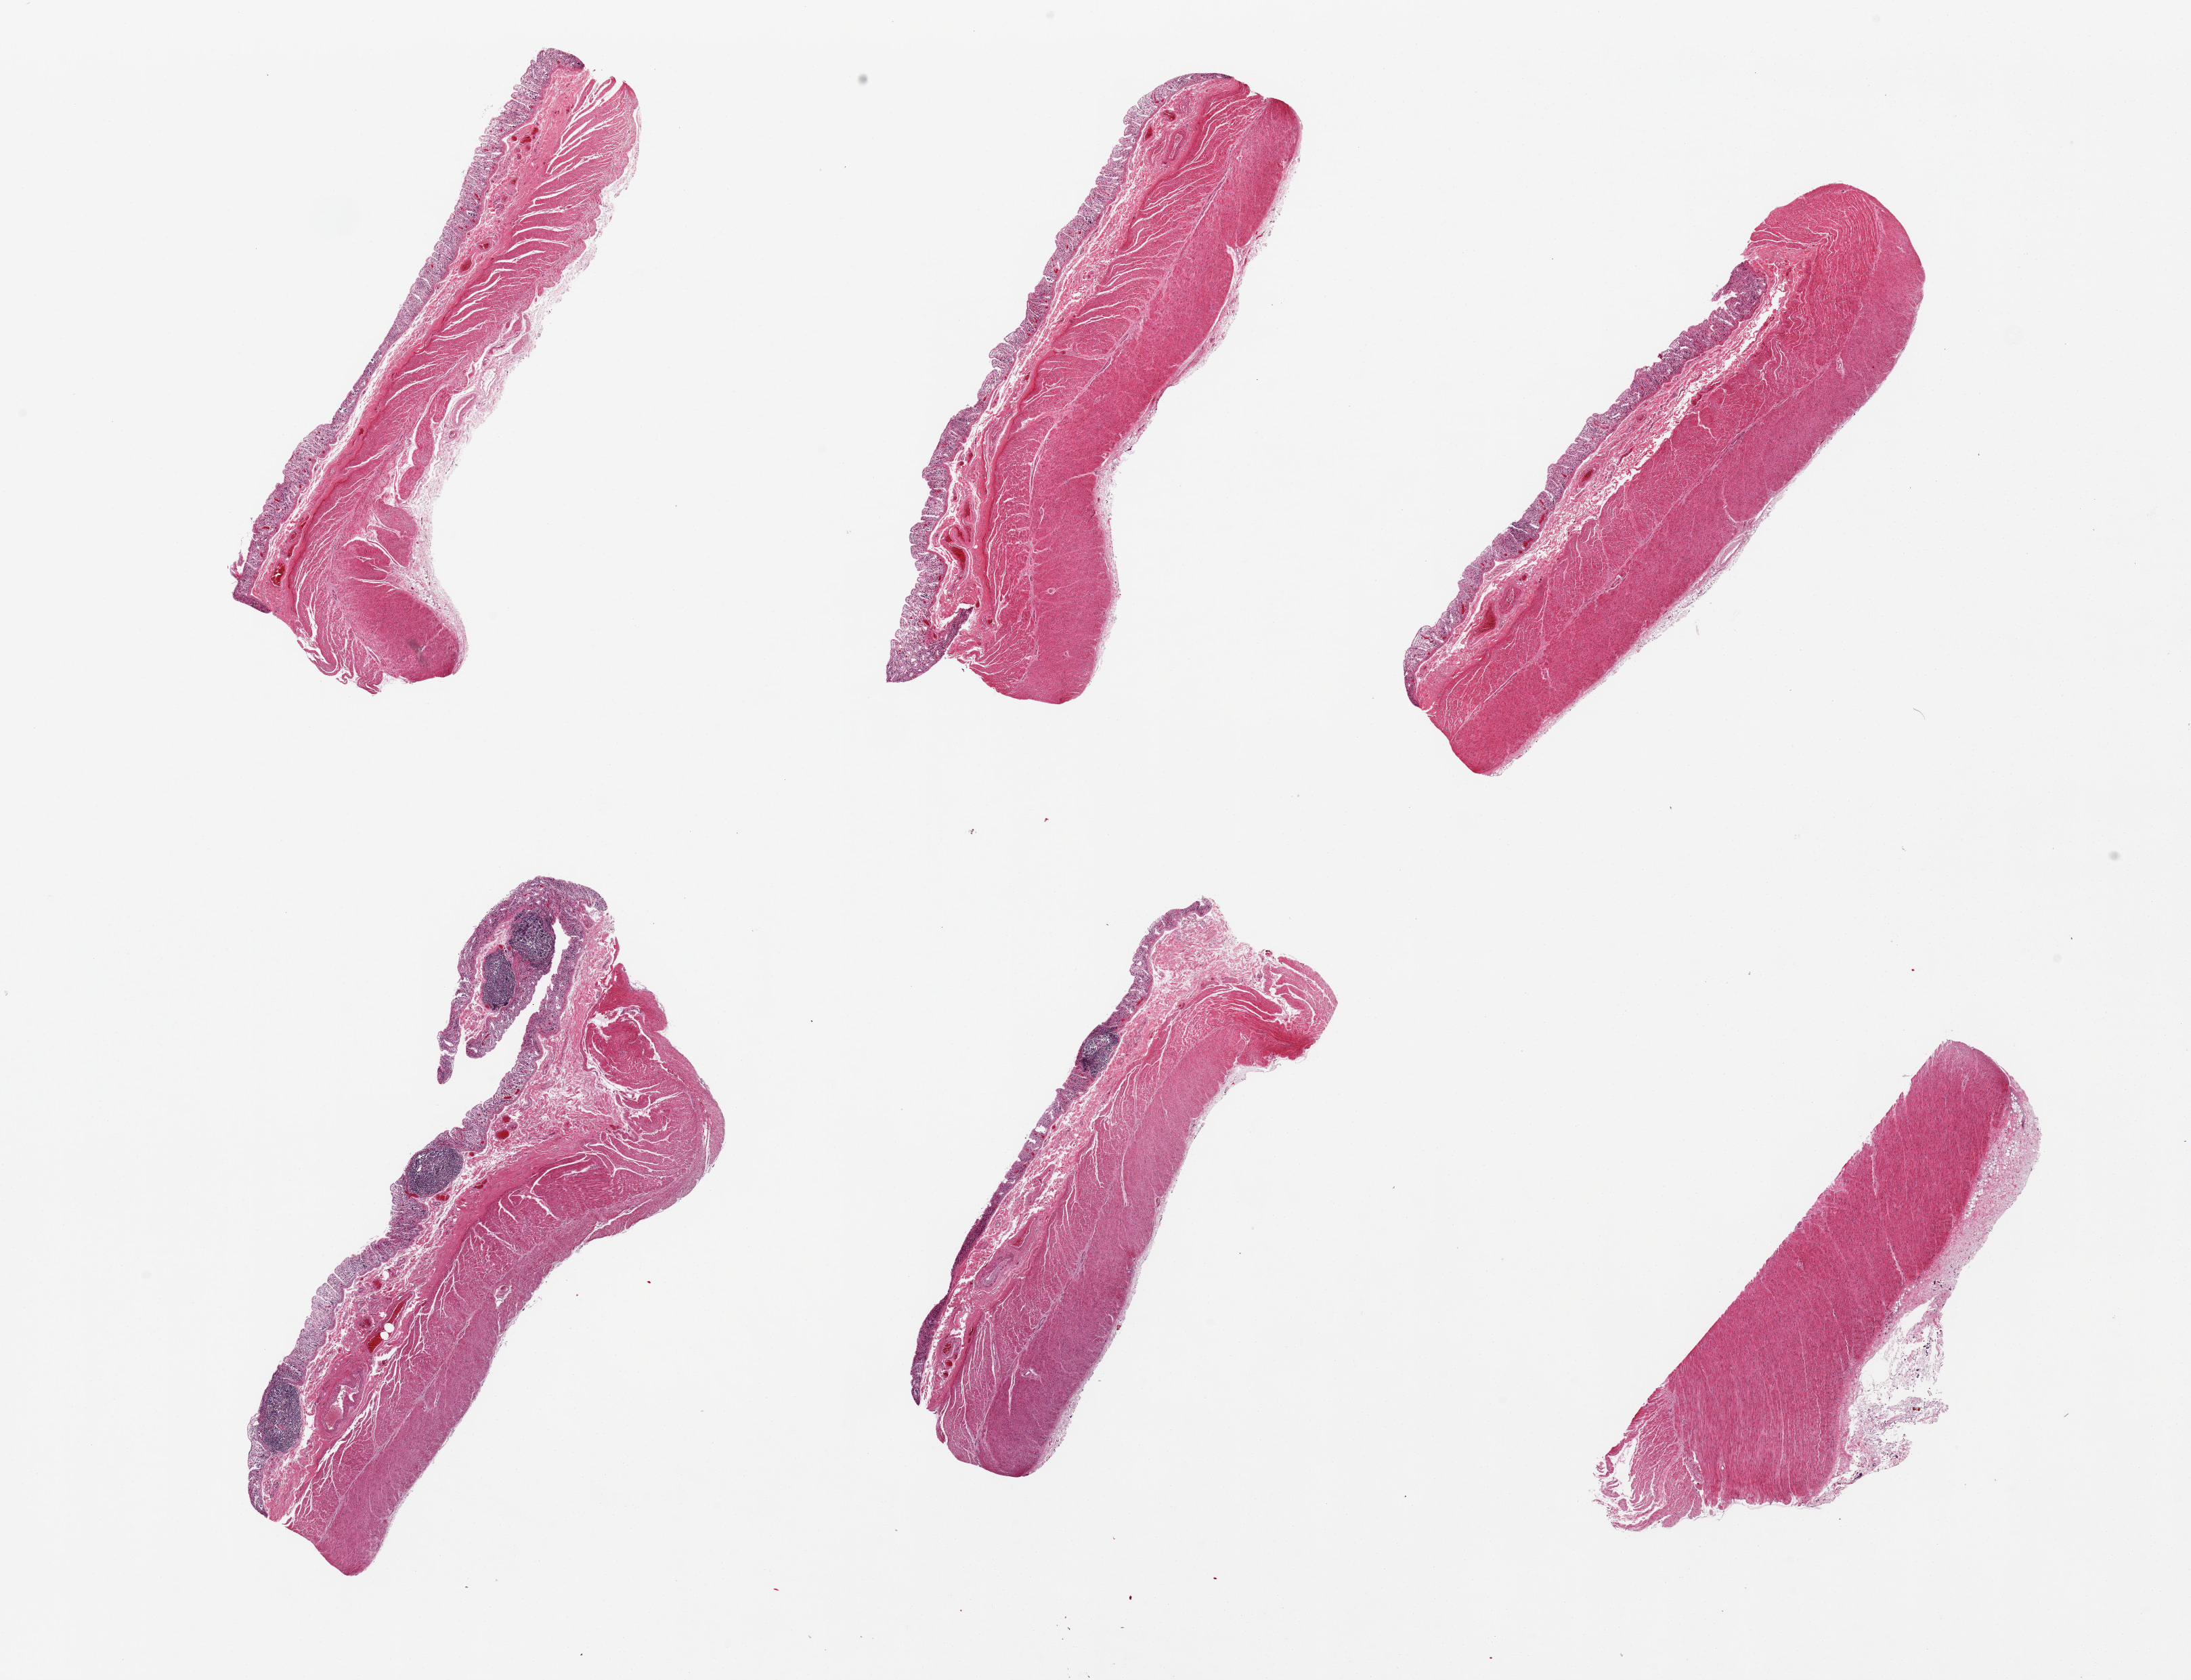
H&E whole-slide image — low-resolution overview of the scanned area, about 25.6 x 19.6 mm; PAXgene-fixed, paraffin-embedded tissue; target tissue: transverse colon; tissue donor sample. Donor sex: male.
Review note (as recorded): 6 pieces; mucosa autolysis=3, muscularis autolysis=2.